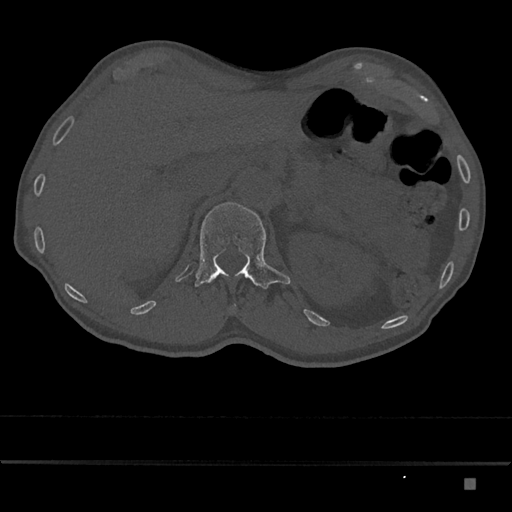
CT including the spine, one axial slice. Slice 555 of 797 in the series (ordered by position). Bone window (W 1800 / L 400 HU). 0.5 mm slice thickness. 512 × 512 image matrix. Male patient, age 72 years. From the clinical record (not read from this slice): primary cancer: prostate.
Structures marked on this image (semi-automatic segmentation, software-assisted and operator-edited):
- L1 vertebra: bounding box [x1, y1, x2, y2] px = [195, 202, 290, 289]
- T12 vertebra: [211, 278, 215, 282]